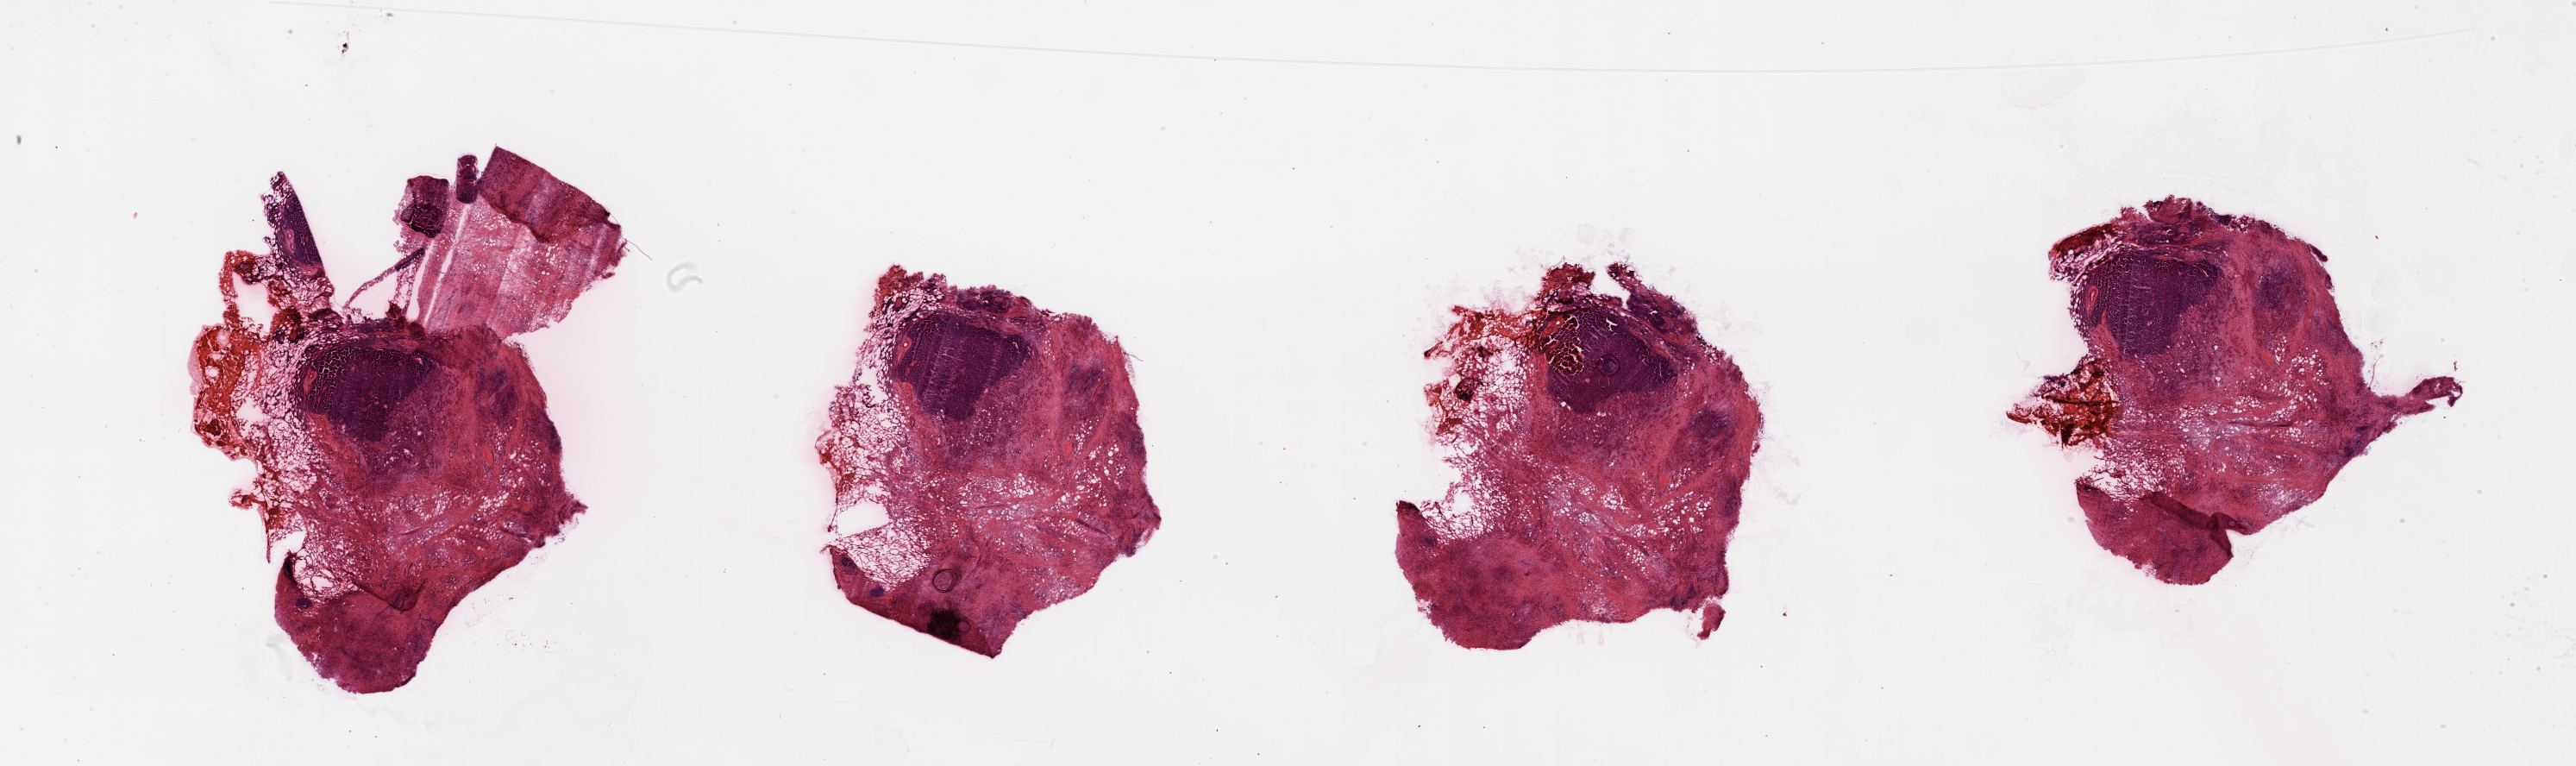
H&E whole-slide image — whole scanned area (about 47.3 x 14.0 mm) shown as a low-resolution overview; tumour tissue sample, sampled site: pancreas. 65-year-old male patient. Histologic grade: G3 (poorly differentiated). Composition of this section per pathologist review: tumour nuclei 50%, necrosis 0%.
AJCC pathologic stage: III. Primary tumour site (as recorded): head. Histologic diagnosis: Infiltrating duct carcinoma, NOS.